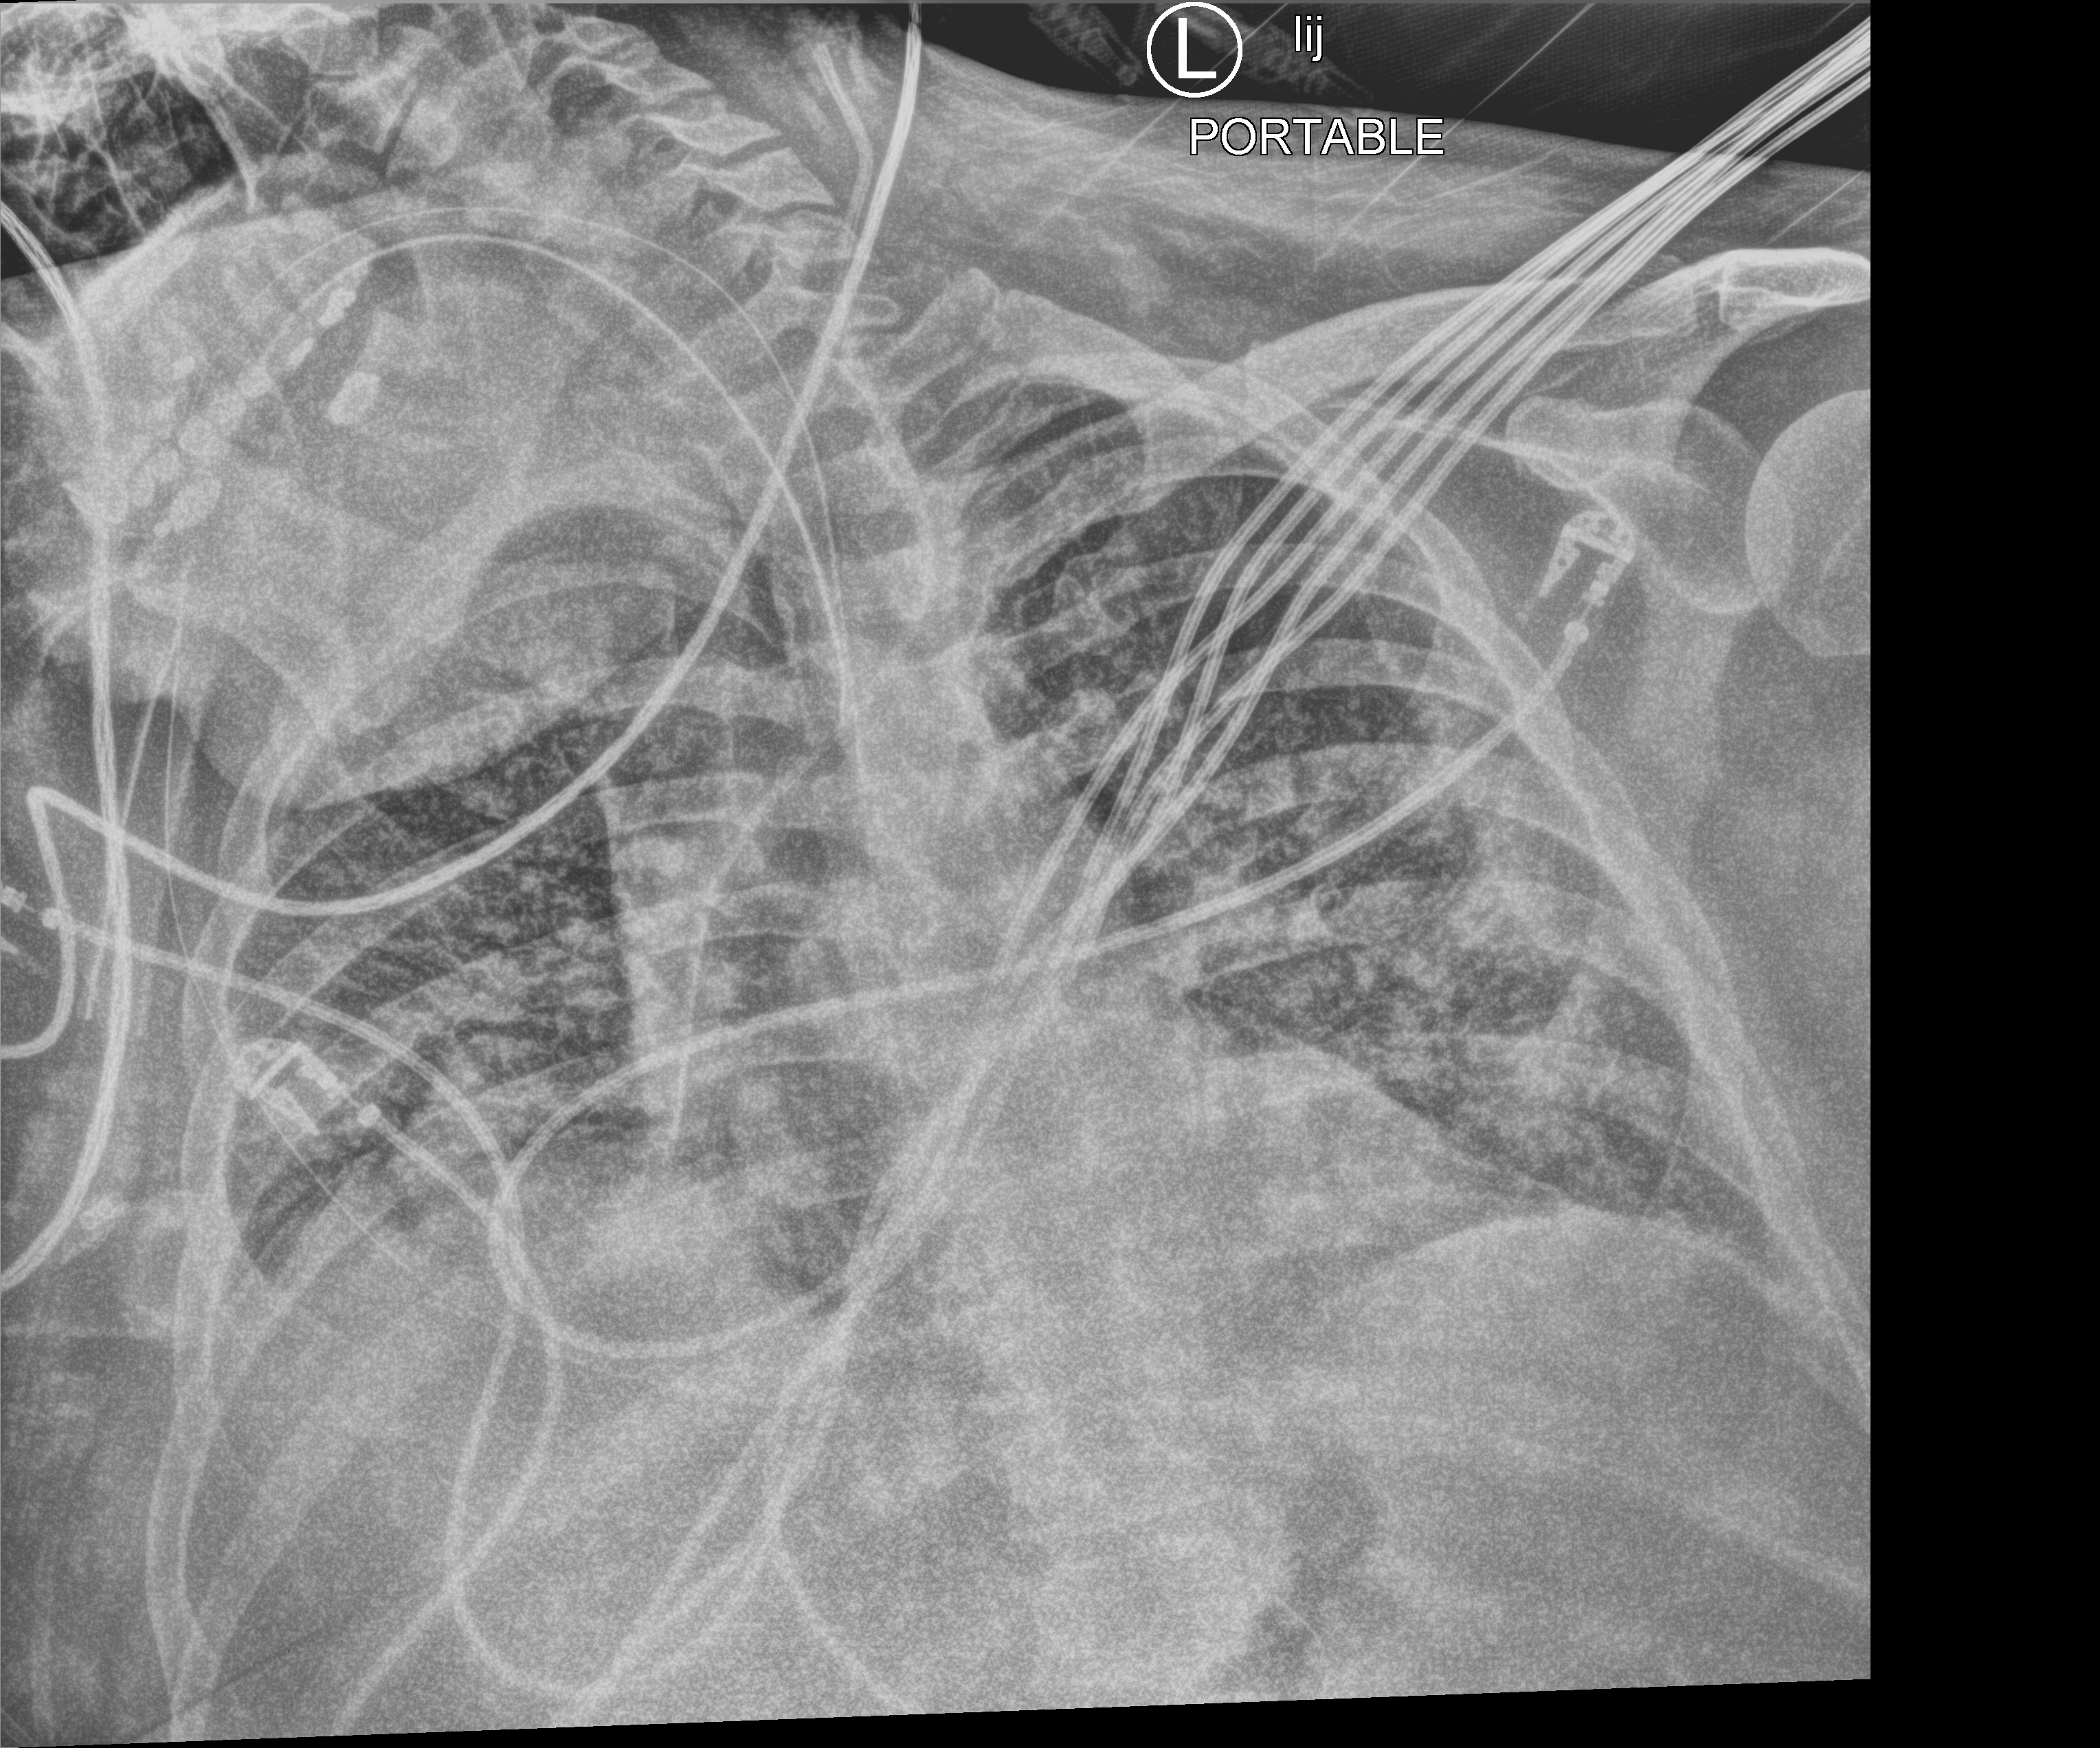
Portable chest radiograph, anteroposterior (AP) projection. Patient hospitalised with COVID-19; male, aged 18–59 years.
Hospital-stay facts (about this admission, not read from this image; timing relative to this image not recorded): mechanically ventilated during this hospital stay: yes; diabetes (admission record): no; admitted to intensive care during this hospital stay: yes.